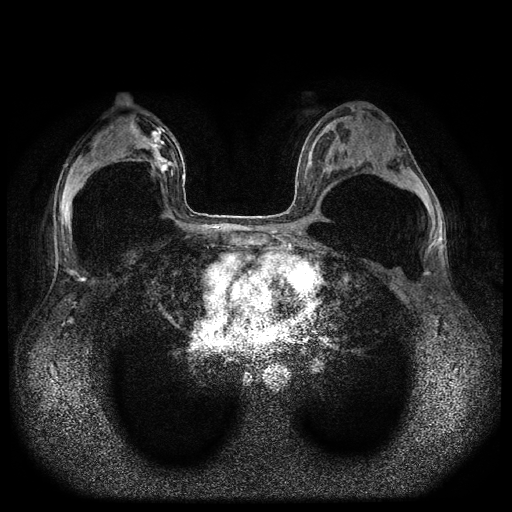
Breast MRI (dynamic contrast-enhanced, multi-phase), one axial slice; slice 49 of 116 in the series (ordered by position); dynamic contrast-enhanced series, time point 2 of 5 at this slice position (early post-contrast); 1.5 T; TE 2.6 ms, TR 5.4 ms; 2 mm slice thickness; 512 × 512 image matrix. Patient: female, 42 years.
Annotated regions visible in this slice (semi-automatically segmented with operator editing):
- breast lesion (labelled 'tumour' in the annotation; benign lesions carry a separate 'benign' label): box from (x=152, y=128) to (x=174, y=178) px